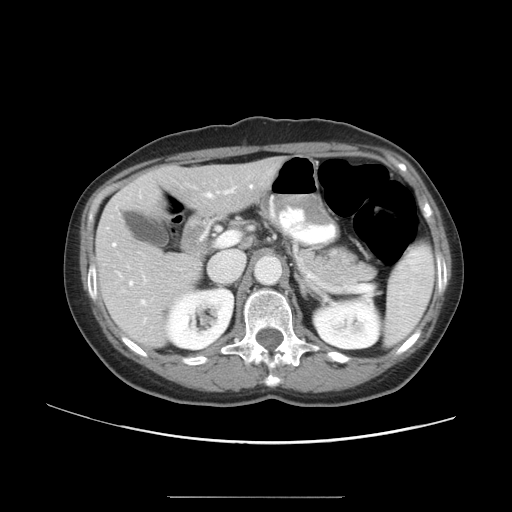
Contrast-enhanced abdominal CT, one axial slice. Slice 27 of 50 in the series (ordered by position). Reconstruction kernel STANDARD. 120 kVp. Intravenous contrast given. Soft-tissue window (W 400 / L 40 HU). 5 mm slice thickness. 512 × 512 image matrix, field of view 389 × 389 mm. Female patient, age 58 years. From the clinical record (not read from this slice): diagnosis: colorectal cancer liver metastases, imaged before liver resection; multiple liver metastases: yes; largest metastasis: 7.3 cm; disease in both lobes: yes.
Outlined on this slice (outlined manually by an expert reader):
- hepatic veins: bounding box <113,185,253,246> (left, top, right, bottom; pixels)
- liver: <98,161,278,346>
- planned liver remnant (the part of the liver to remain after resection): <165,161,277,214>
- portal vein (with intrahepatic branches): <129,192,227,304>